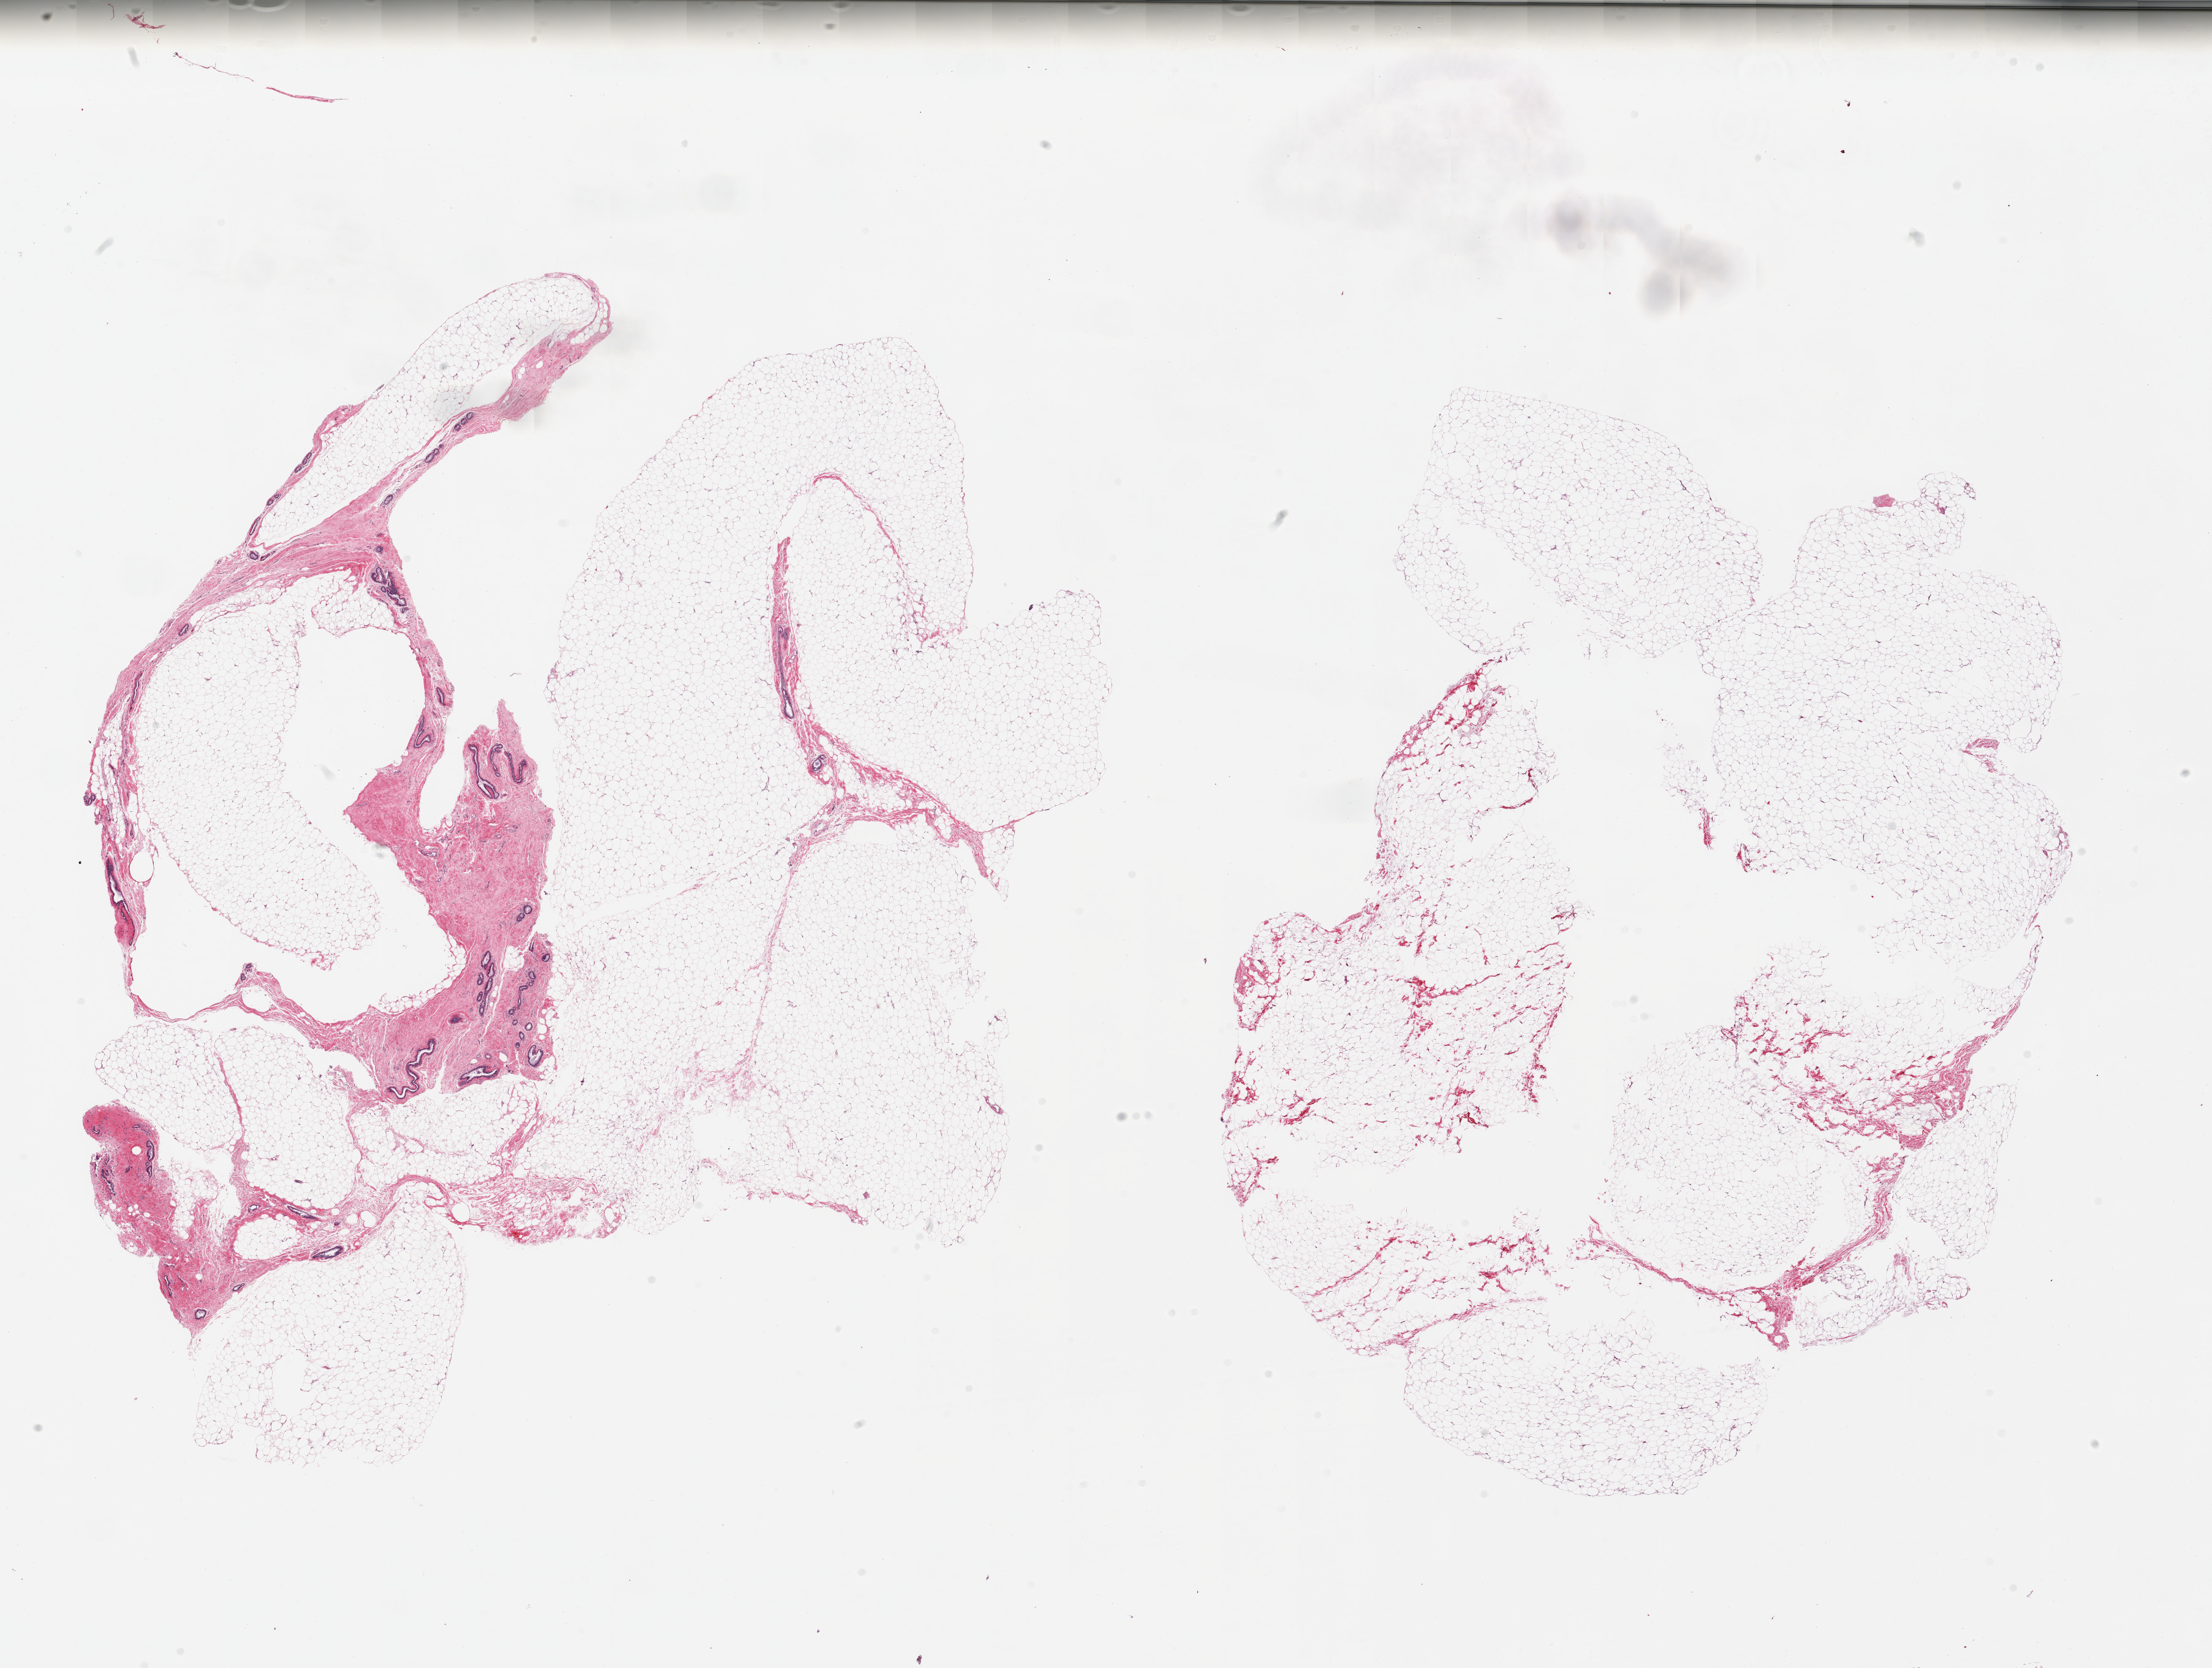
H&E whole-slide image, low-resolution overview of the scanned area, about 28.5 x 21.5 mm. PAXgene-fixed paraffin-embedded (PFPE) section. Sampled site (target tissue): breast. Tissue donor sample. Male donor.
- pathologist's review note for this sample: 2 pieces, mainly fibroadipose elements; trace ductal elements present